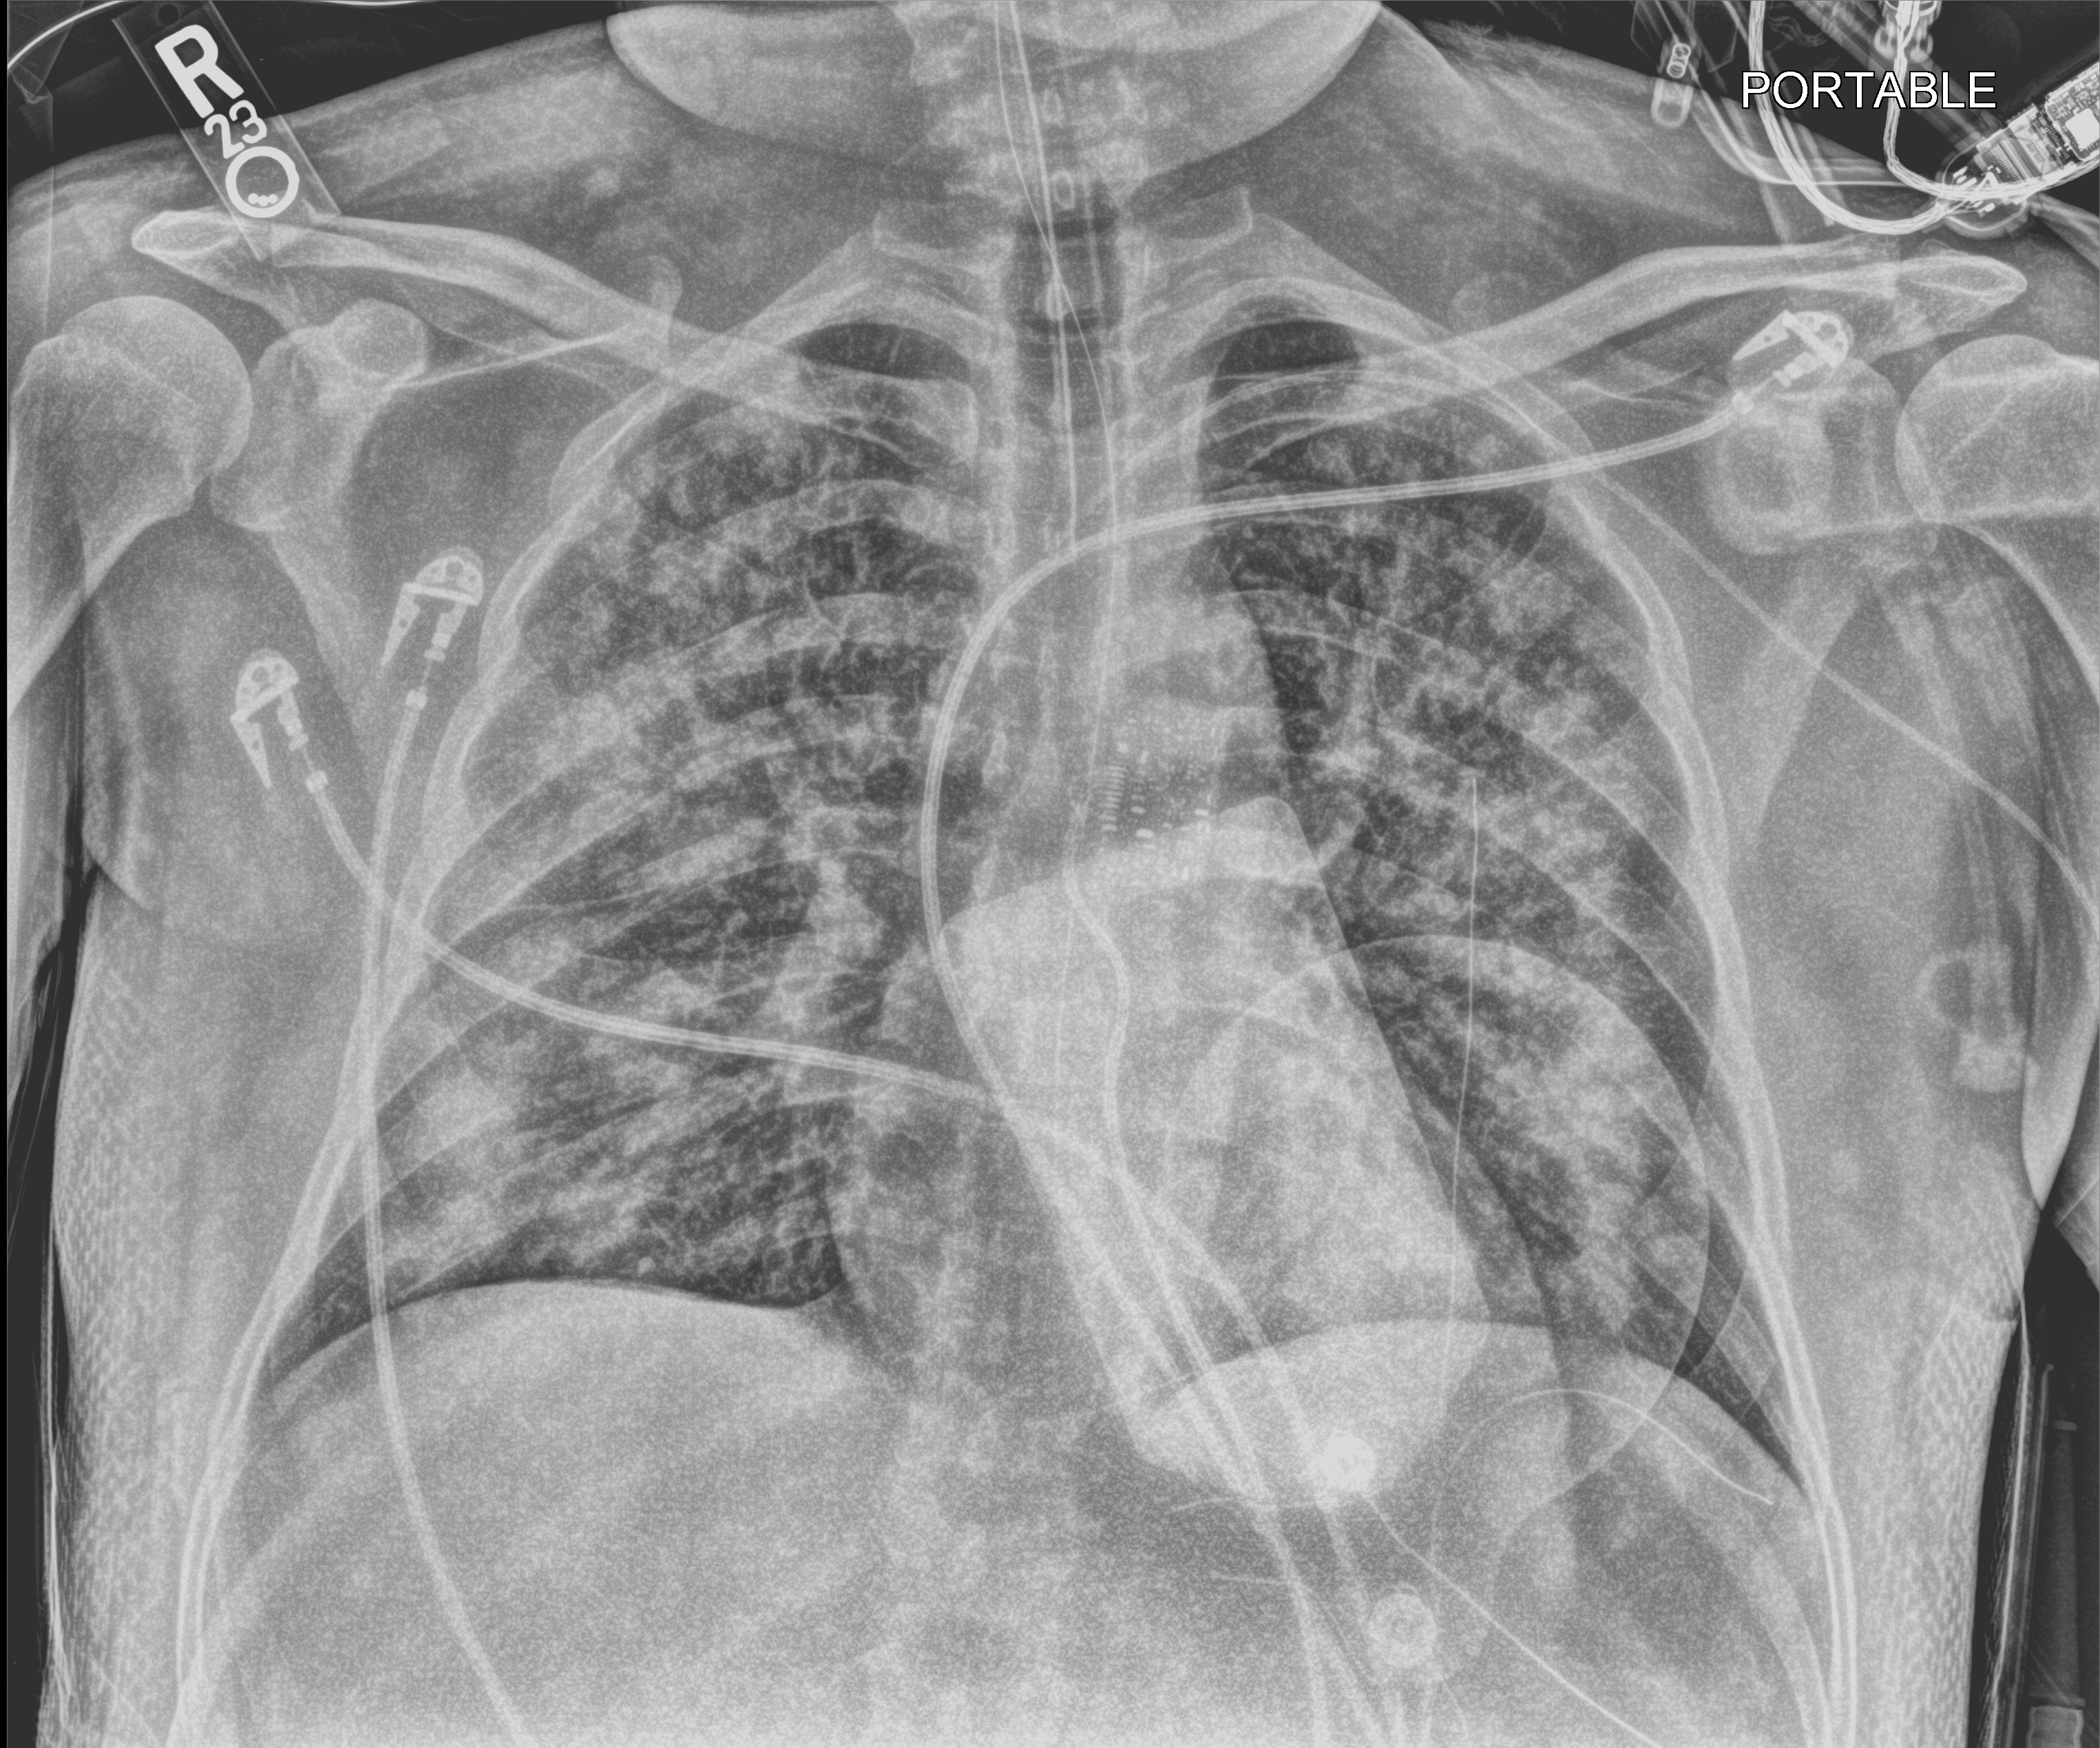
Chest X-ray (portable), anteroposterior (AP) projection. Adult patient hospitalised with COVID-19, age 18–59 years.
Hospital-stay facts (about this admission, not read from this image; timing relative to this image not recorded): mechanically ventilated during this hospital stay: yes; COPD (admission record): no; admitted to intensive care during this hospital stay: no.